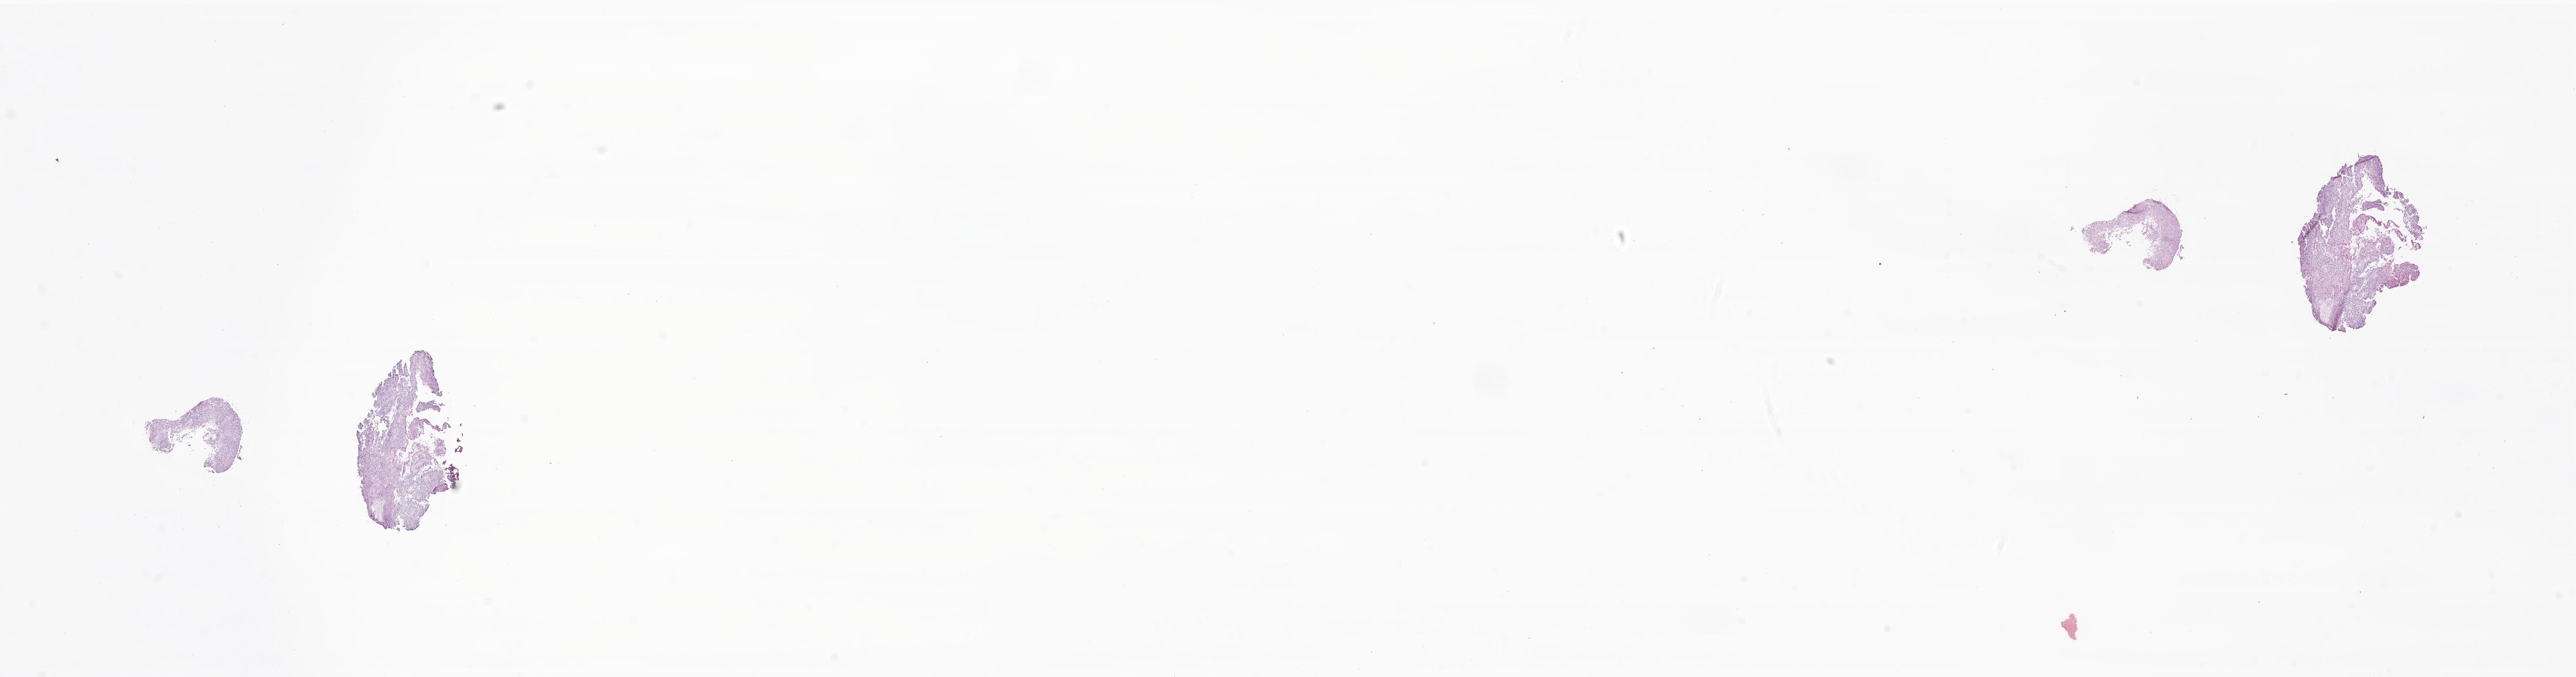
Digitized H&E-stained section of tumor tissue from the brain — a low-resolution overview of the entire scanned area, about 33.7 x 8.9 mm. Frozen section. Patient female; age 556 days.
• recorded diagnosis: Neoplasm, malignant